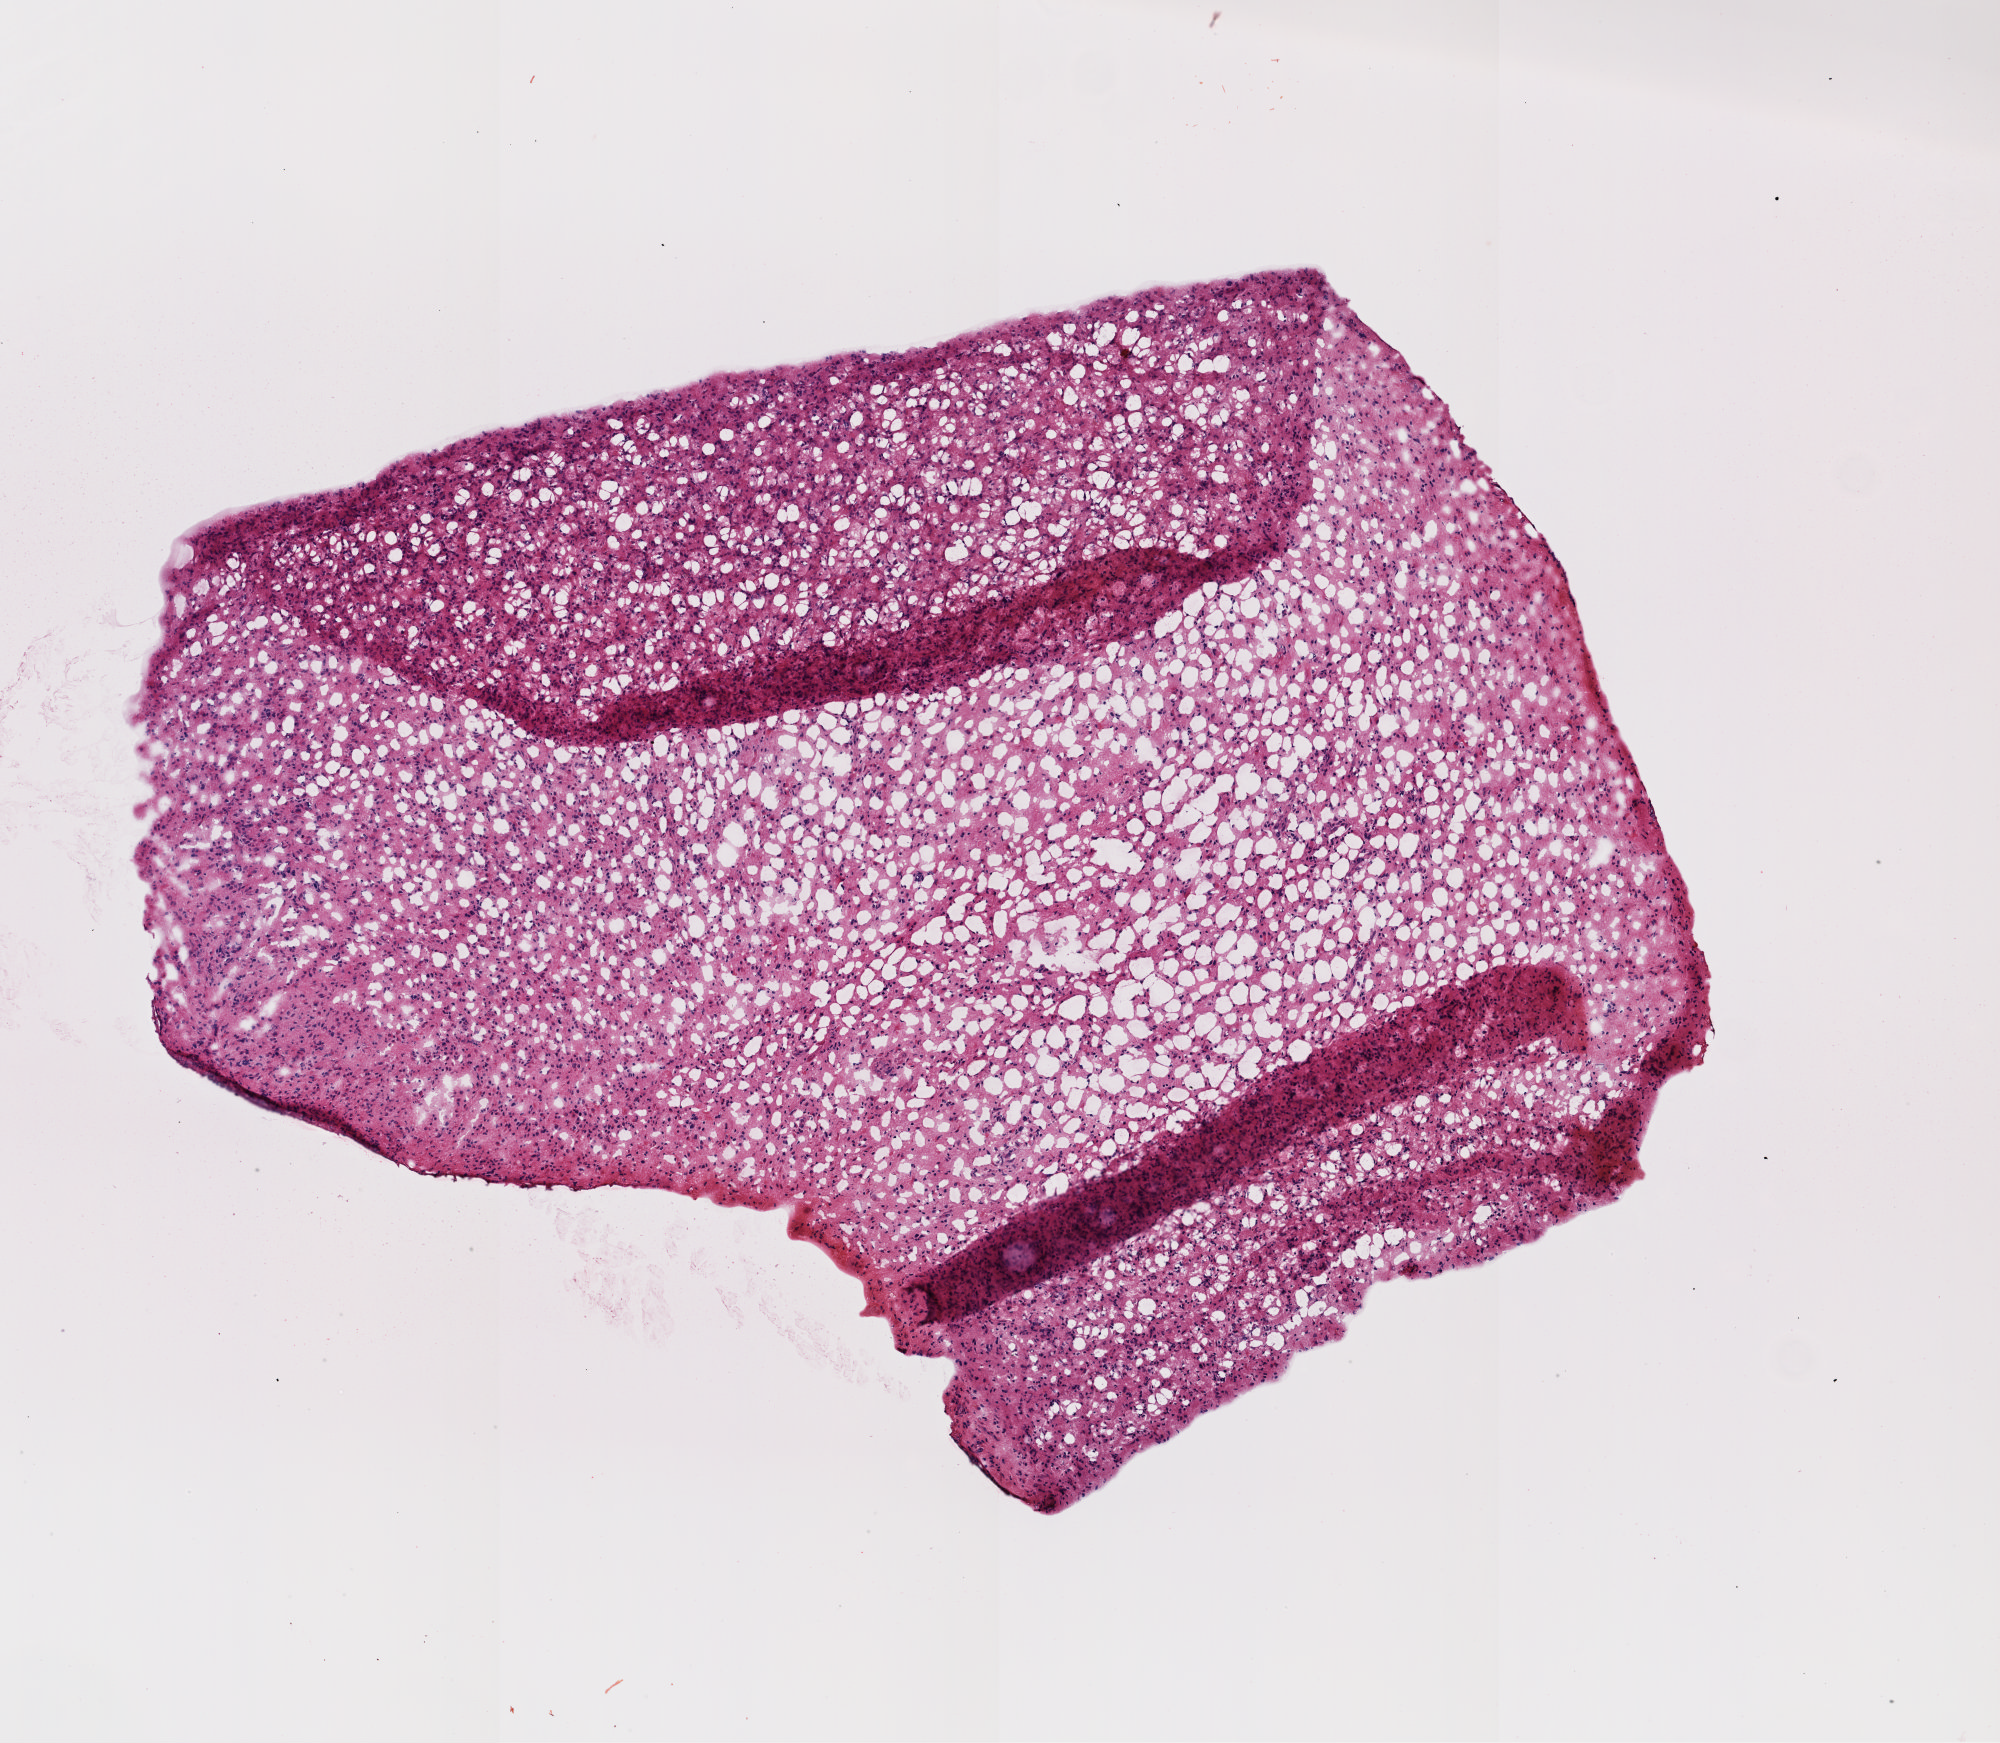
Digitized Hematoxylin and eosin (H&E) stained tissue section (whole slide) — low-resolution overview of the scanned area, about 4.0 x 3.5 mm; frozen section from the top of the tissue portion; primary tumour sample from the brain. Female patient; age at initial diagnosis 78 years. Composition of this section per pathologist review: tumour cells 100%, tumour nuclei 70%, normal cells 0%, stromal cells 0%, necrosis 0%.
Diagnosis: Glioblastoma.